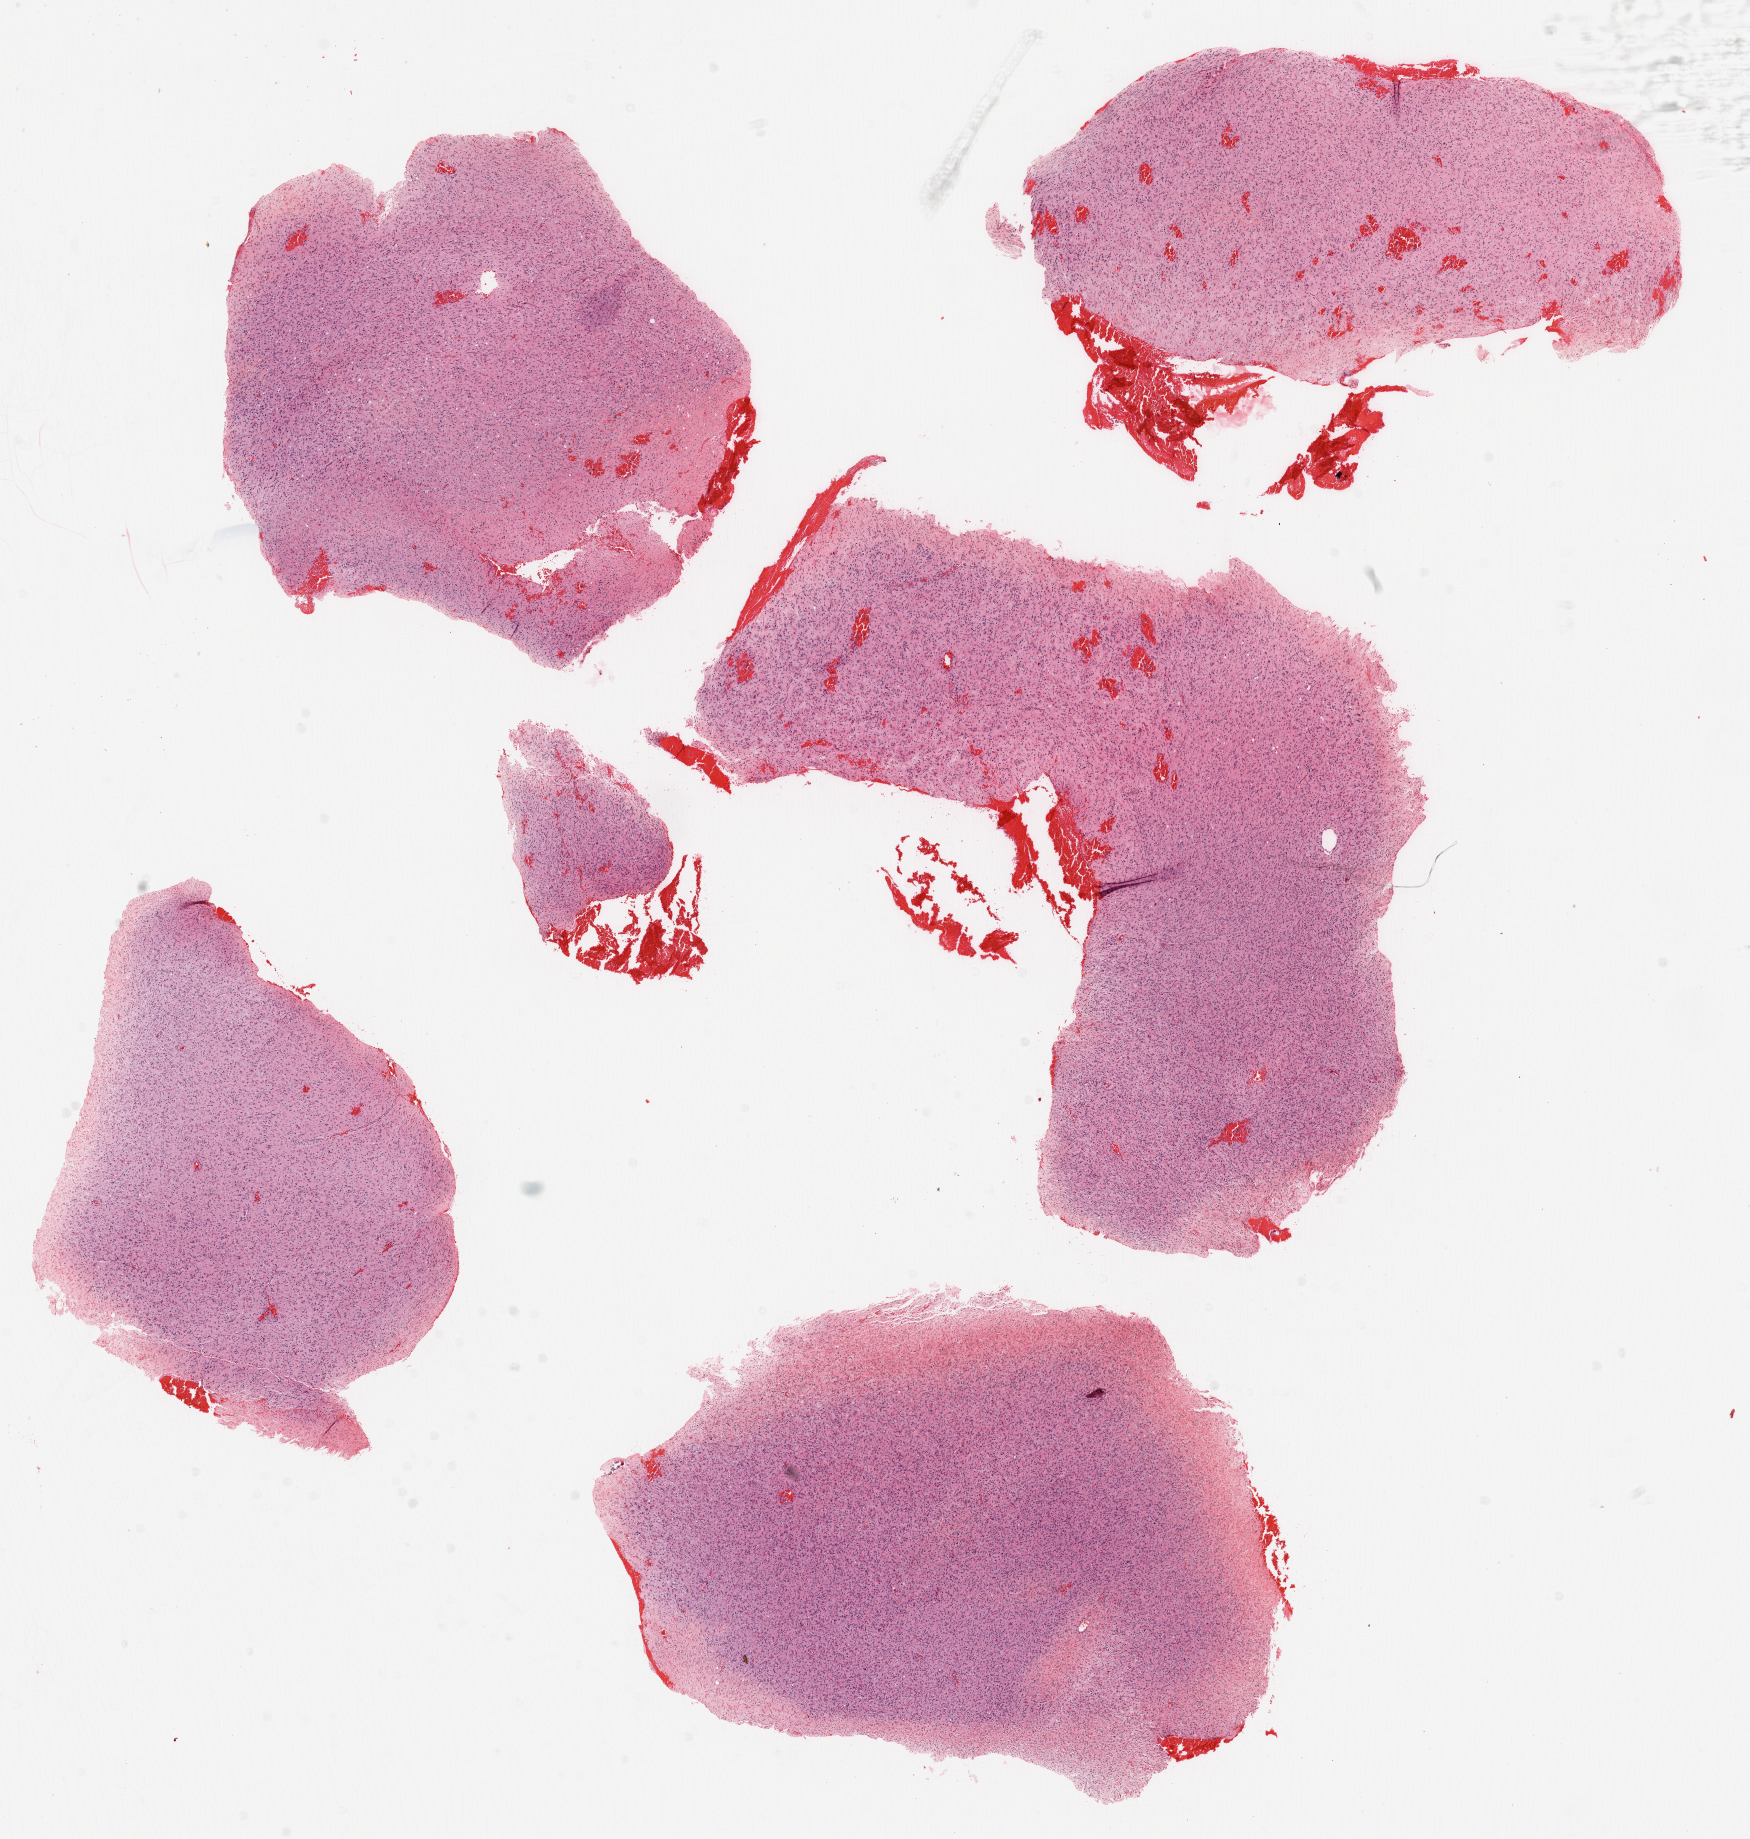
H&E-stained whole-slide image, low-resolution overview of the scanned area, about 14.0 x 14.8 mm. Formalin-fixed paraffin-embedded (FFPE) diagnostic section. Brain, primary tumour sample. Male, age 51 years at initial diagnosis.
Histologic diagnosis: Glioblastoma.